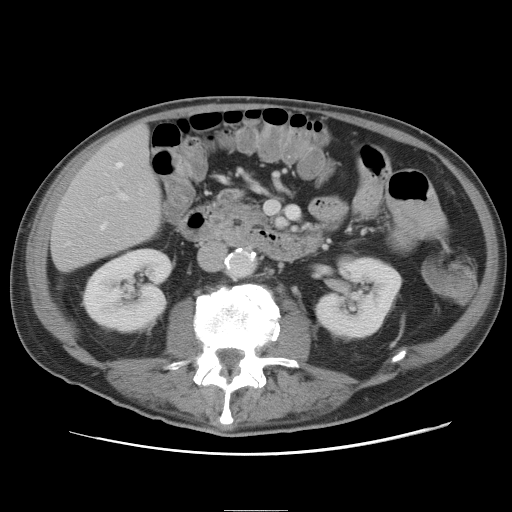
Contrast-enhanced abdominal CT, one axial slice; slice 19 of 89 in the series (ordered by position); 120 kVp; intravenous contrast given; soft-tissue window (W 400 / L 40 HU); 5 mm slice thickness; 512 × 512 image matrix. Male patient, age 69 years. From the clinical record (not read from this slice): diagnosis: colorectal cancer liver metastases, imaged before liver resection; multiple liver metastases: no; largest metastasis: 8.5 cm; disease in both lobes: no.
Outlined on this slice (manually delineated by an expert):
- hepatic veins: bounding box <102,162,123,229> (left, top, right, bottom; pixels)
- liver: <52,125,162,271>
- planned liver remnant (the part of the liver to remain after resection): <53,125,162,271>
- portal vein (with intrahepatic branches): <120,192,128,200>